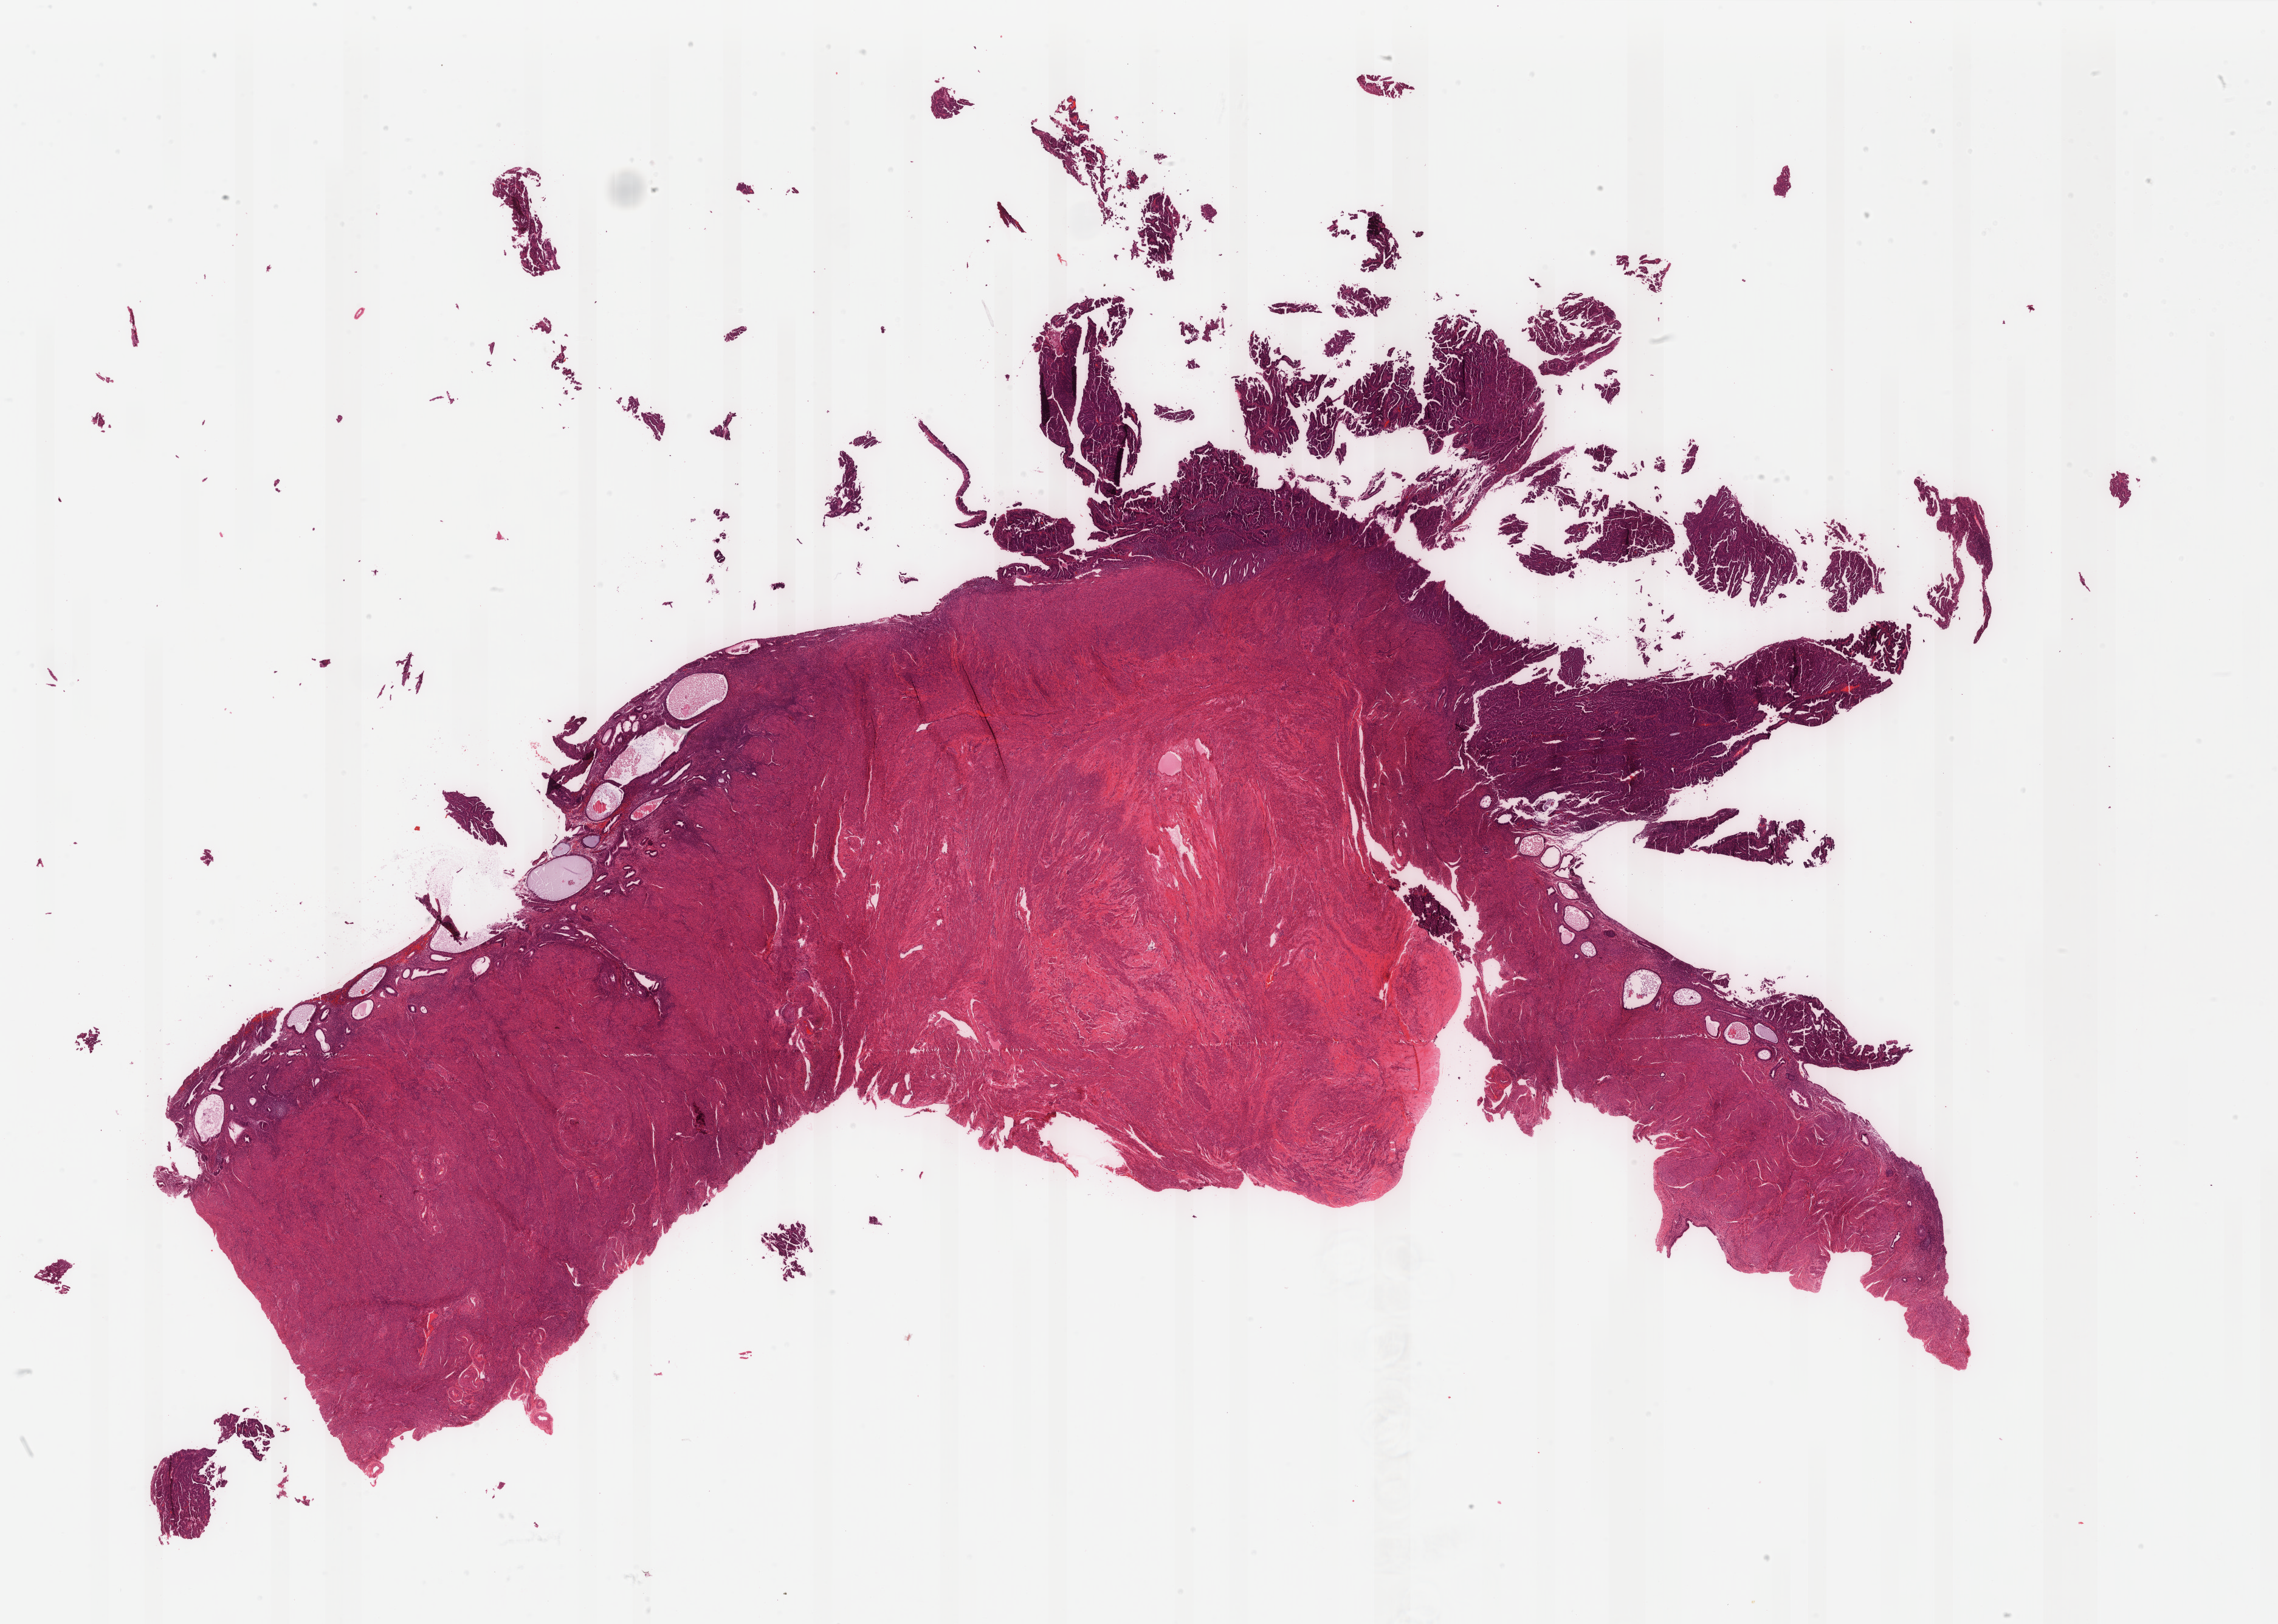
H&E-stained whole-slide image, a low-resolution overview of the entire scanned area, about 29.7 x 21.2 mm (slide scanned at 40x); FFPE section; uterus, primary tumour sample. Patient: female, age at initial diagnosis 60 years. Histologic grade: G3 (poorly differentiated).
Lymph nodes positive (case pathology): 0 of 2 examined. FIGO stage: IA. Pathologic diagnosis: Serous cystadenocarcinoma, NOS (endometrium).